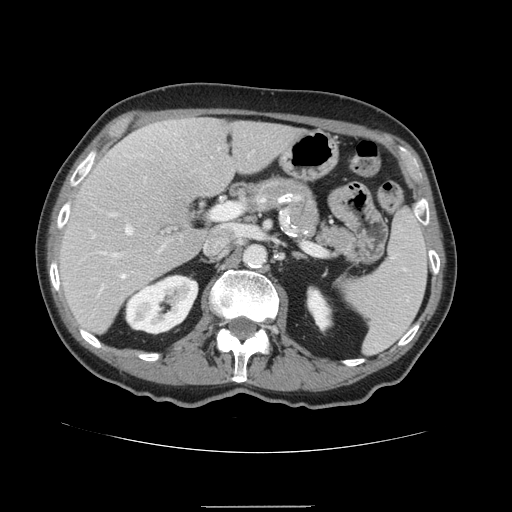
Contrast-enhanced abdominal CT, one axial slice. Slice 86 of 168 in the series (ordered by position). 120 kVp. Soft-tissue window (W 400 / L 40 HU). 2.5 mm slice thickness. 512 × 512 image matrix, field of view 386 × 386 mm. Male patient, age 74 years. Case-level facts recorded for this patient, not image findings: diagnosis: colorectal cancer liver metastases, imaged before liver resection; multiple liver metastases: no; largest metastasis: 14.5 cm.
Structures marked on this image (manually delineated by an expert):
- hepatic veins: bounding box <122,225,133,277> (left, top, right, bottom; pixels)
- liver: <59,118,307,334>
- planned liver remnant (the part of the liver to remain after resection): <59,121,306,334>
- portal vein (with intrahepatic branches): <97,204,239,261>
- liver metastasis: <172,176,196,206>